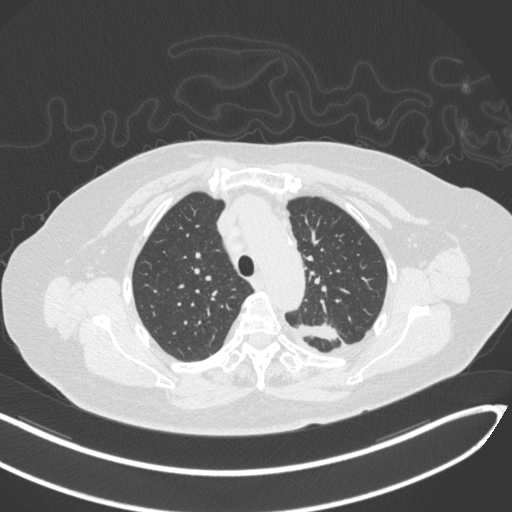
Chest CT, one axial slice; position 240 of 270 along the scan axis; lung window (W 1500 / L -600 HU); 1 mm slice thickness; 512 × 512 image matrix, field of view 400 × 400 mm. Female patient, age 76 years. From the clinical record (not read from this slice): clinical TNM (as recorded): T1c N0 M0.
Outlined on this slice (rectangle marked by the reading radiologist):
- lung tumour (recorded histology: adenocarcinoma): bounding box <298,320,340,348> (left, top, right, bottom; pixels)